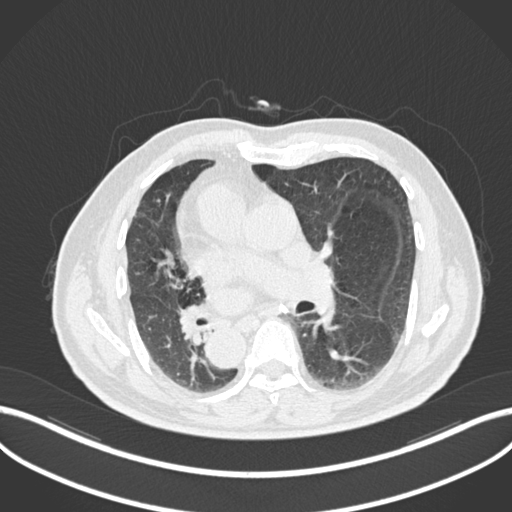
Chest CT, one axial slice; position 113 of 206 along the scan axis; reconstruction kernel B30f; 120 kVp; lung window (W 1500 / L -600 HU); 1 mm slice thickness; 512 × 512 image matrix, field of view 400 × 400 mm. Male patient, age 67 years. From the clinical record (not read from this slice): clinical TNM (as recorded): T2a N0 M0.
Outlined on this slice (rectangle marked by the reading radiologist):
- lung tumour (recorded histology: squamous cell carcinoma): bounding box <175,305,212,346> (left, top, right, bottom; pixels)